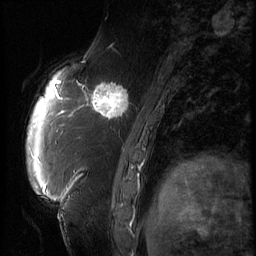
Breast MRI (dynamic contrast-enhanced), one sagittal slice. Slice 21 of 66 in the series (ordered by position). 3 images stored at this slice position (order not interpretable as contrast timing). 1.5 T. TE 4.2 ms, TR 9 ms. 2.5 mm slice thickness. 256 × 256 image matrix. Female patient, age 57 years. From the clinical record (not read from this slice): setting: breast cancer imaged before/during neoadjuvant chemotherapy; receptor status: triple-negative.
Outlined on this slice (semi-automatic segmentation, software-assisted and operator-edited):
- analysis volume of interest (the breast-tissue region the enhancement analysis was run in; not a lesion): bounding box [x1, y1, x2, y2] px = [86, 74, 138, 129]
- tumour enhancement mask (voxels above the 140 % enhancement threshold inside the analysis volume of interest): [86, 81, 132, 122]